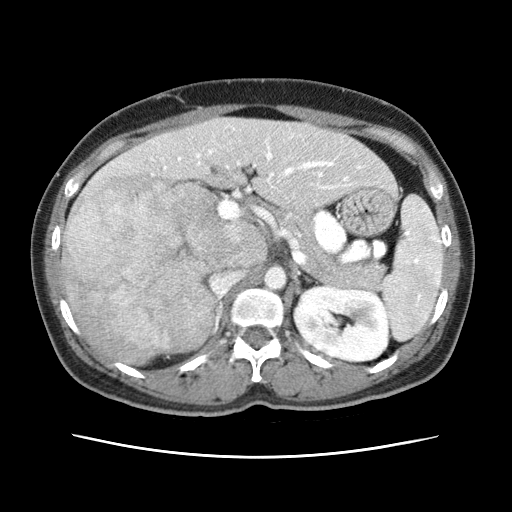
Contrast-enhanced abdominal CT (liver protocol), one axial slice; slice 31 of 79 in the series (ordered by position); reconstruction kernel STANDARD; 120 kVp; soft-tissue window (W 400 / L 40 HU); 2.5 mm slice thickness; 512 × 512 image matrix, field of view 340 × 340 mm. Case-level facts recorded for this patient, not image findings: diagnosis: hepatocellular carcinoma (patient treated with transarterial chemoembolisation; whether this scan precedes or follows treatment is not stated here); TNM stage (as recorded): Stage-I; Child-Pugh class: A; tumour differentiation: moderately differentiated; tumour nodularity: uninodular.
Structures marked on this image (semi-automatically segmented with operator editing):
- abdominal aorta: bounding box <264,268,286,289> (left, top, right, bottom; pixels)
- liver parenchyma outside the tumour (the mass and vessels are separate outlines, so this box may not span the whole liver): <62,117,388,362>
- mass: <61,173,234,361>
- liver vessels: <112,138,362,189>